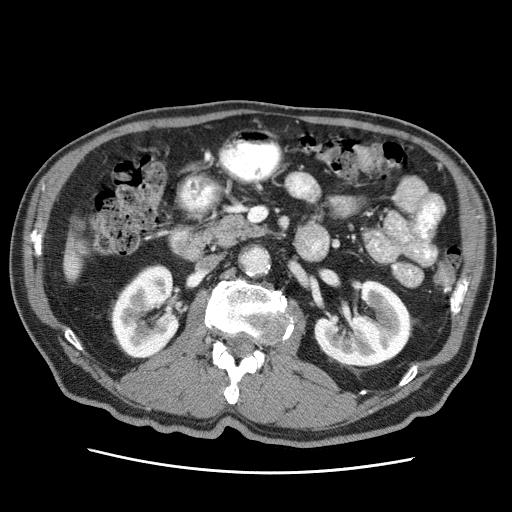
Contrast-enhanced abdominal CT (liver protocol), one axial slice. Slice 6 of 75 in the series (ordered by position). Reconstruction kernel STANDARD. 120 kVp. Soft-tissue window (W 400 / L 40 HU). 512 × 512 image matrix, field of view 360 × 360 mm. From the clinical record (not read from this slice): diagnosis: hepatocellular carcinoma (patient treated with transarterial chemoembolisation; whether this scan precedes or follows treatment is not stated here); TNM stage (as recorded): Stage-IIIA; Child-Pugh class: A; tumour differentiation: well differentiated.
Annotated regions visible in this slice (semi-automatic segmentation, software-assisted and operator-edited):
- liver parenchyma outside the tumour (the mass and vessels are separate outlines, so this box may not span the whole liver): bounding box [x1, y1, x2, y2] px = [64, 241, 84, 280]